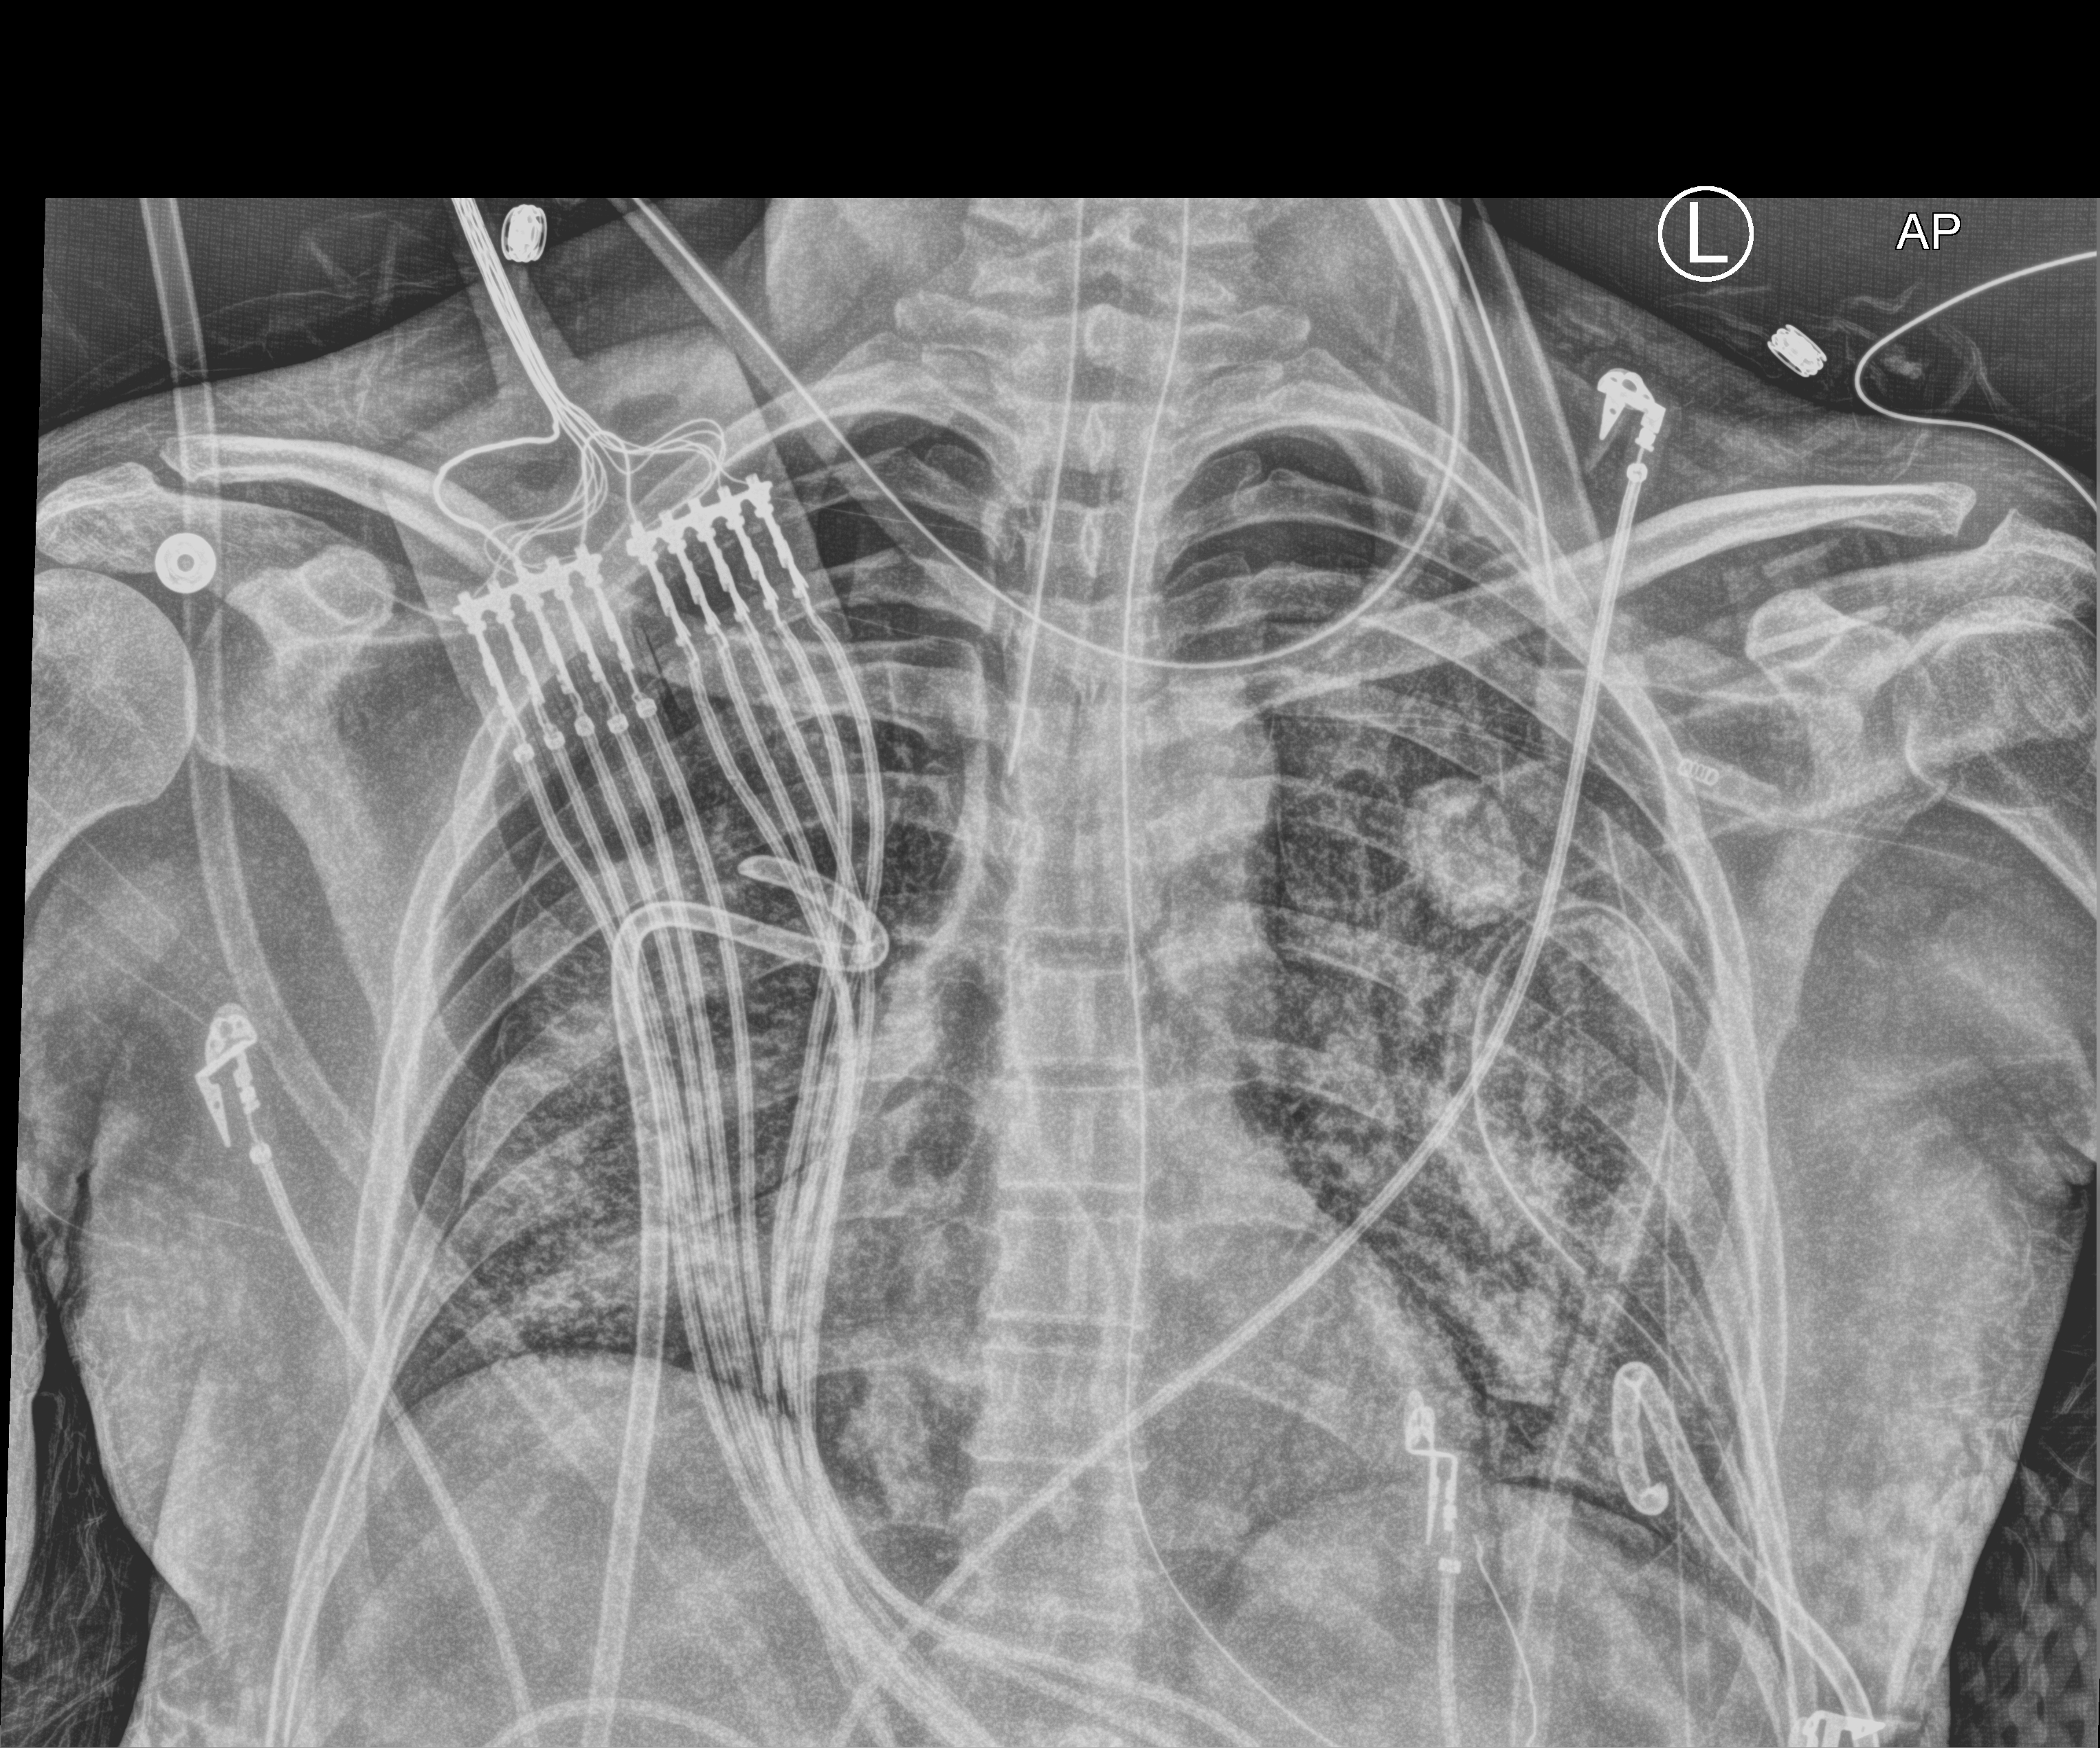
Chest X-ray (portable), anteroposterior (AP) projection. Patient hospitalised with COVID-19, aged 18–59 years.
From the hospital-stay record, not from the radiograph (when in the stay this image was taken is not recorded):
- admitted to intensive care during this hospital stay: yes
- smoking status (admission record): never